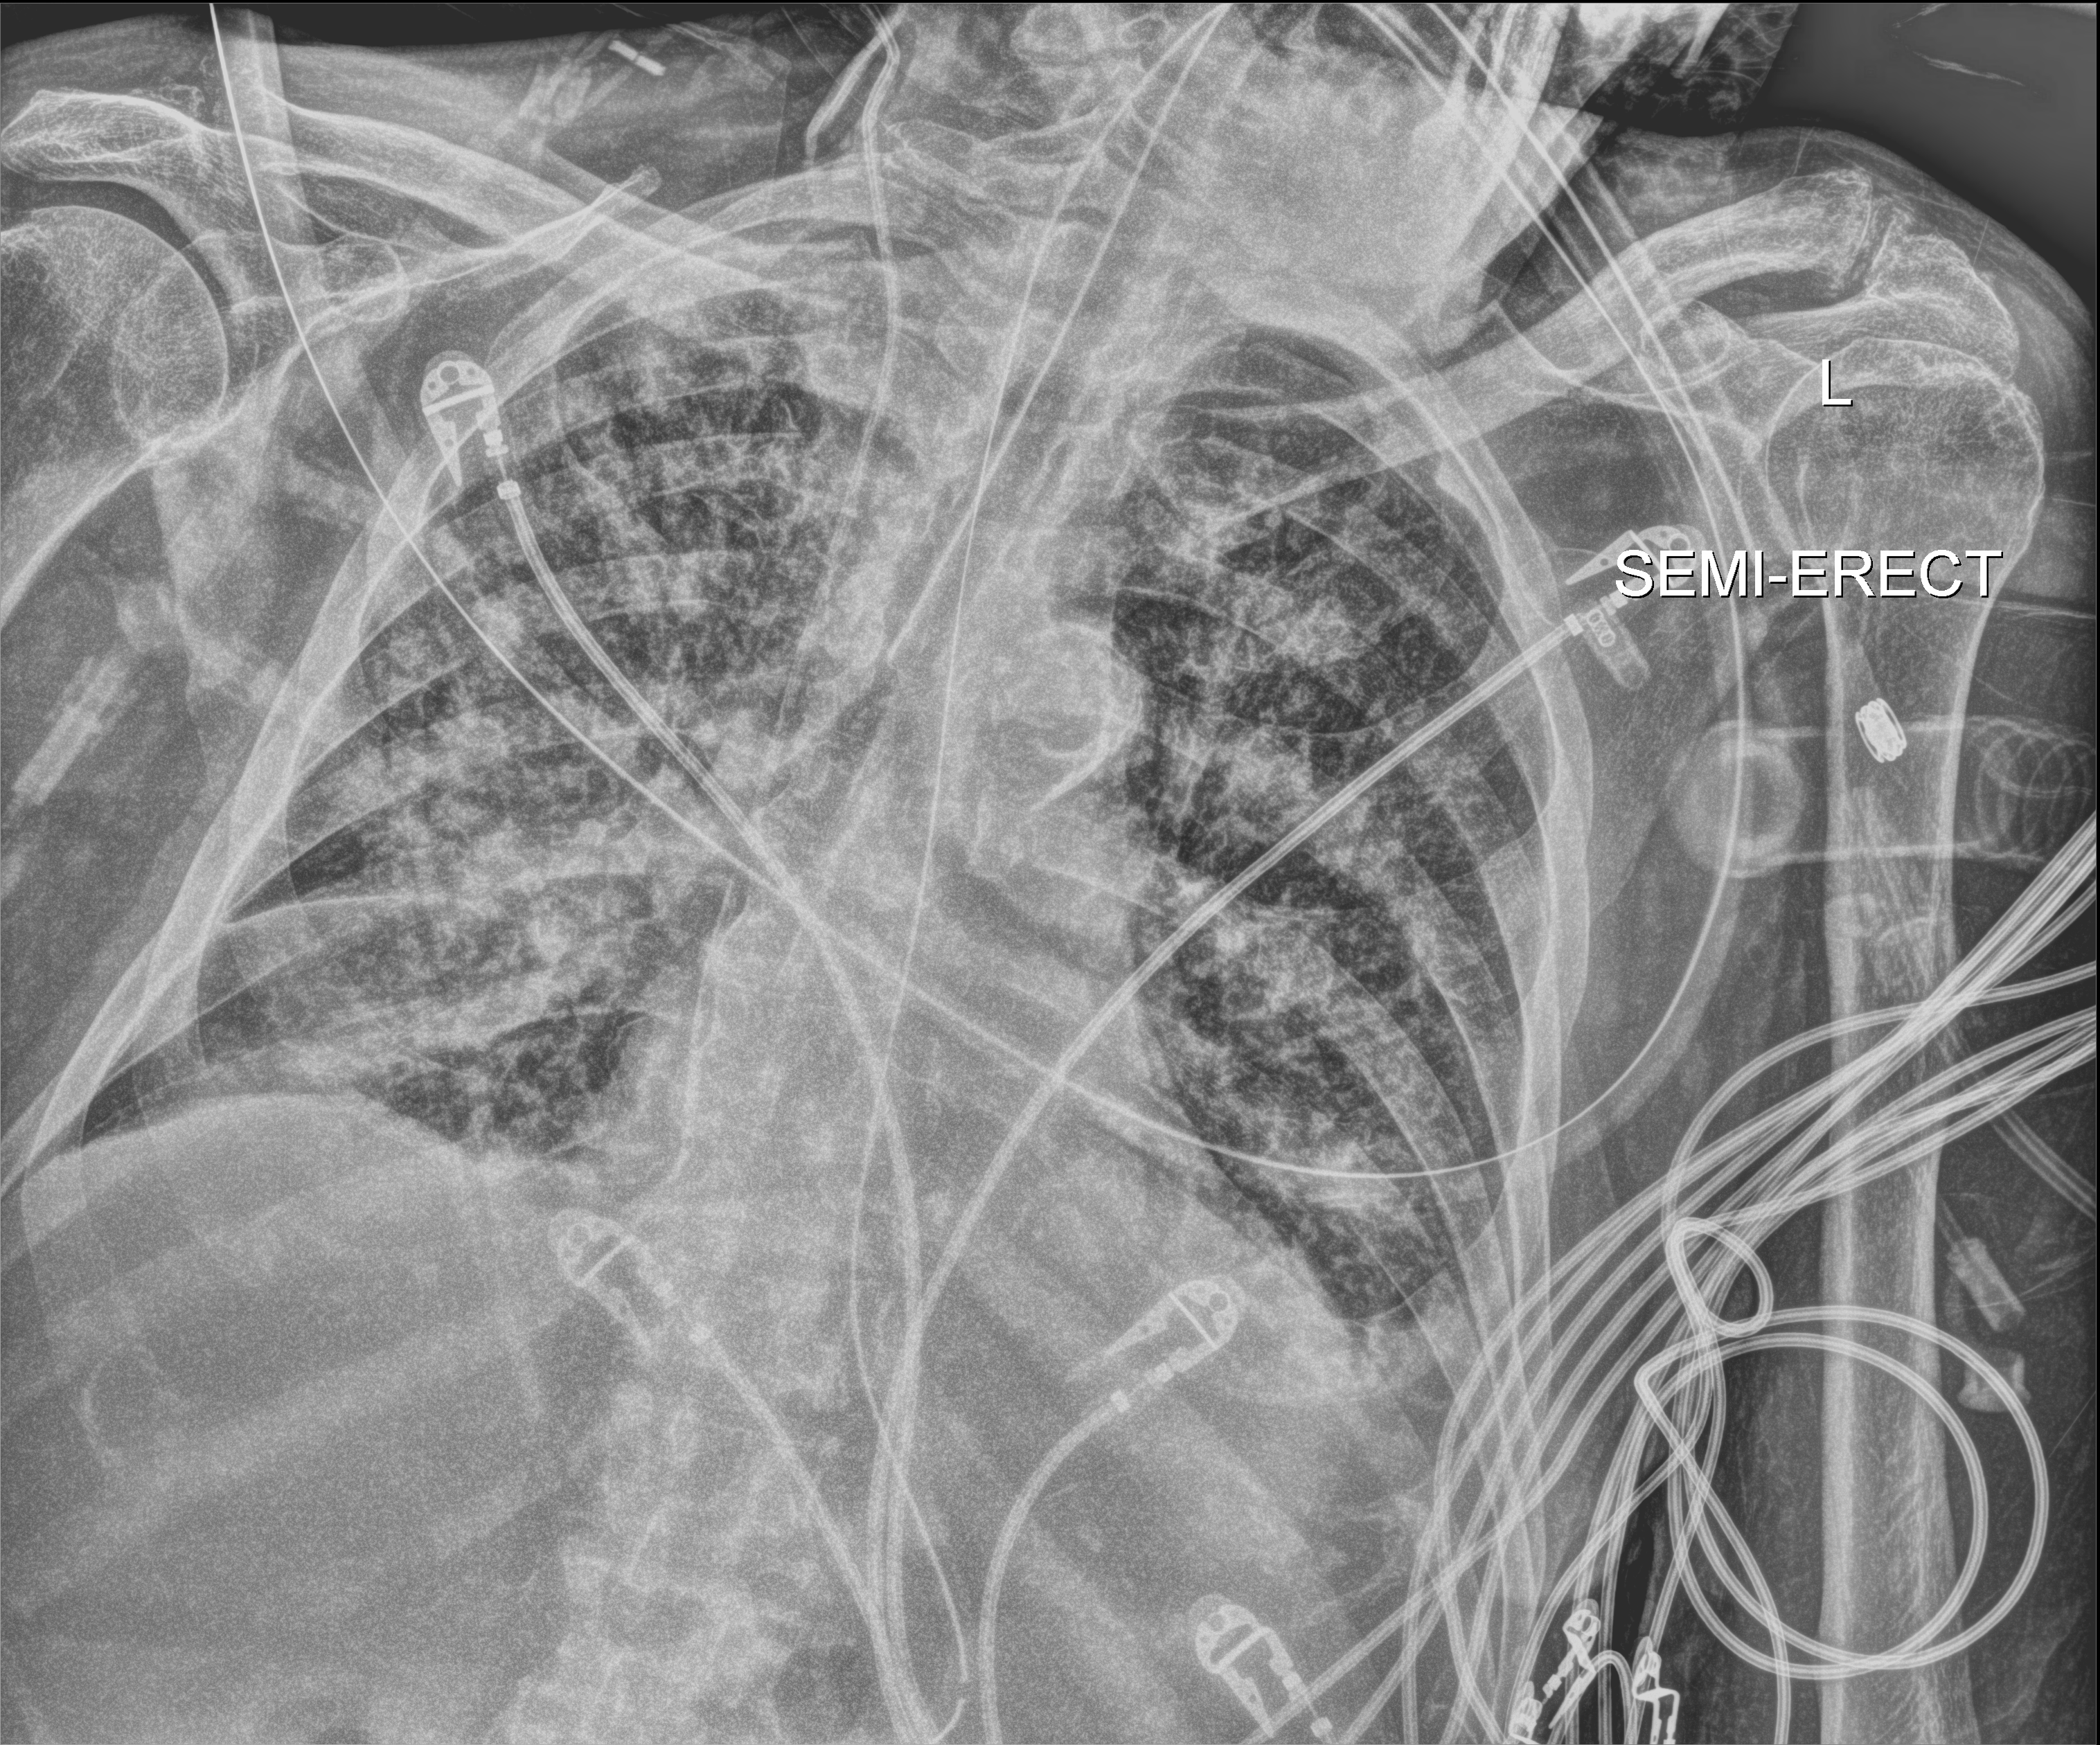
Bedside chest radiograph (digital radiography); anteroposterior (AP) projection. Patient hospitalised with COVID-19; male, aged 75–90 years.
Hospital-stay facts (about this admission, not read from this image; timing relative to this image not recorded): mechanically ventilated during this hospital stay: yes.